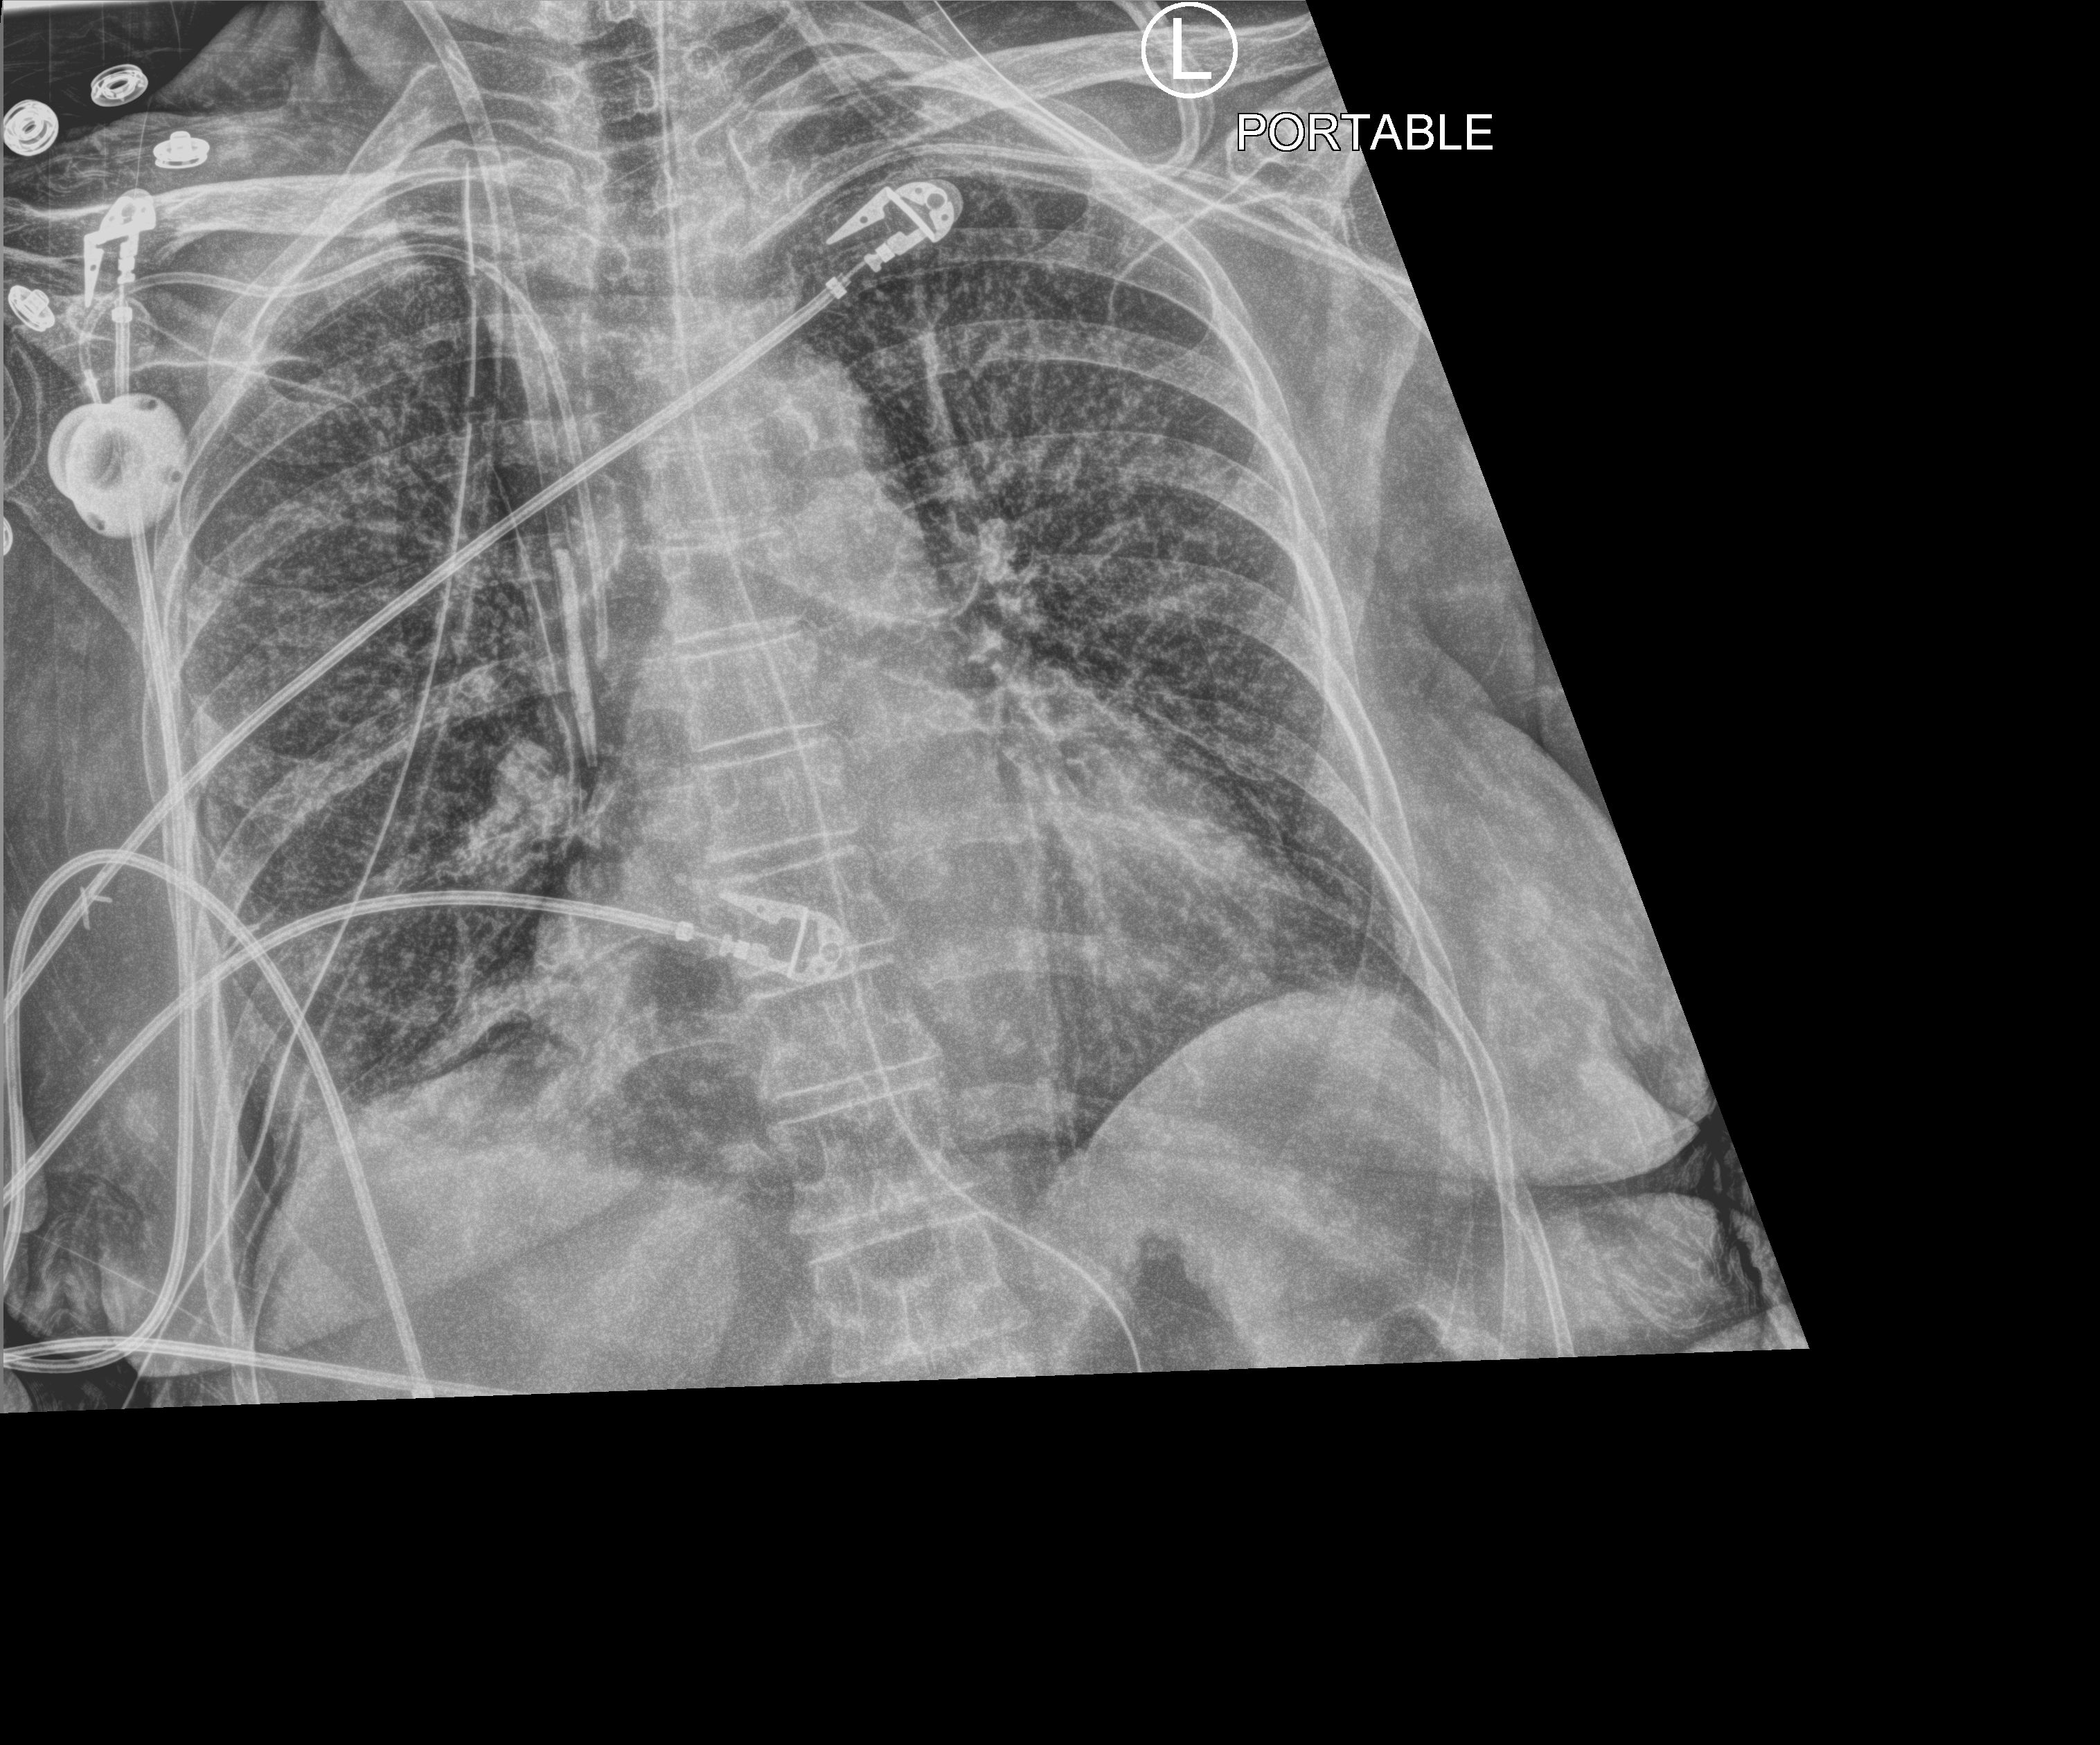
Bedside chest radiograph (computed radiography). Female patient hospitalised with COVID-19, age 60–74 years.
Admission-level facts for this patient (not findings on this image; timing relative to this image not recorded):
- COPD (admission record): no